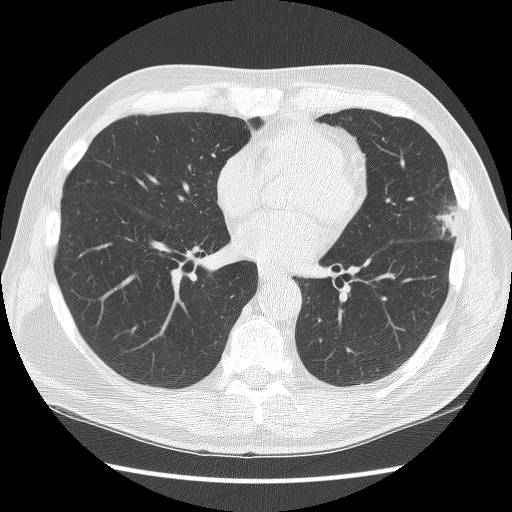
Low-dose screening chest CT, axial slice; third screening round (two years after baseline); lung window (W 1500 / L -600 HU); 2.5 mm slice thickness; lung (sharp) reconstruction kernel (BONE); slice 71 of 134 in the series; 512 × 512 image matrix, field of view 350 × 350 mm. Male, age 67 years at enrolment. Former smoker at enrolment.
Expert reader's lesion annotation, bounding box [x1, y1, x2, y2] px = [409, 187, 472, 259]. Screening reader's record for this exam (one nodule recorded; not confirmed to be the boxed lesion): non-calcified nodule or mass ≥4 mm, left upper lobe, 22 × 17 mm, poorly defined margins, soft tissue attenuation, pre-existing on the prior screen: yes; interval growth: yes. Later outcome: lung cancer diagnosed 72 days after this screen — squamous cell carcinoma, NOS, left upper lobe, moderately differentiated (G2), stage IB (AJCC 6th edition), 25 mm at pathology.